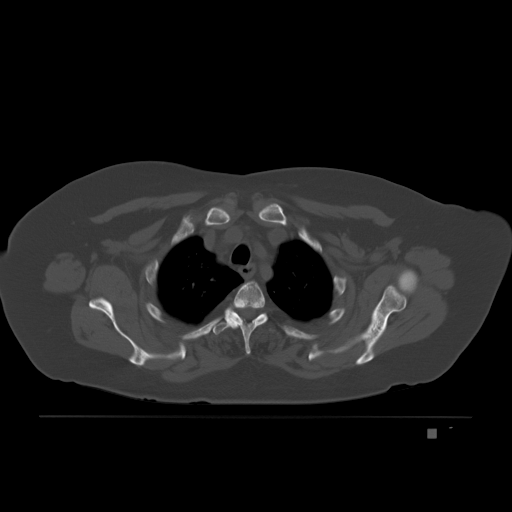
CT including the spine, one axial slice. Slice 164 of 221 in the series (ordered by position). Bone window (W 1800 / L 400 HU). 3 mm slice thickness. 512 × 512 image matrix, field of view 474 × 474 mm. Patient: female, 63 years. Case-level facts recorded for this patient, not image findings: primary cancer: breast.
Structures marked on this image (semi-automatically segmented with operator editing):
- T3 vertebra: bounding box (x1, y1, x2, y2) in pixels: (215, 312, 267, 335)